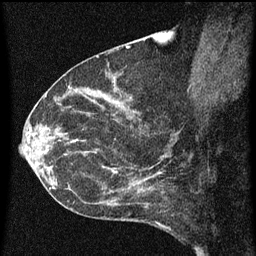
Breast MRI (dynamic contrast-enhanced), one sagittal slice; position 31 of 60 along the scan axis; dynamic contrast-enhanced series, image 2 of 3 at this slice position (ordered by acquisition); 1.5 T; TE 4.2 ms, TR 8 ms; 2 mm slice thickness; 256 × 256 image matrix, field of view 180 × 180 mm. Patient: female, 54 years.
Outlined on this slice (semi-automatic segmentation, software-assisted and operator-edited):
- analysis volume of interest (the breast-tissue region the enhancement analysis was run in; not a lesion): bounding box [x1, y1, x2, y2] px = [49, 138, 164, 209]
- tumour enhancement mask (voxels above the 70 % enhancement threshold inside the analysis volume of interest): [50, 140, 162, 207]